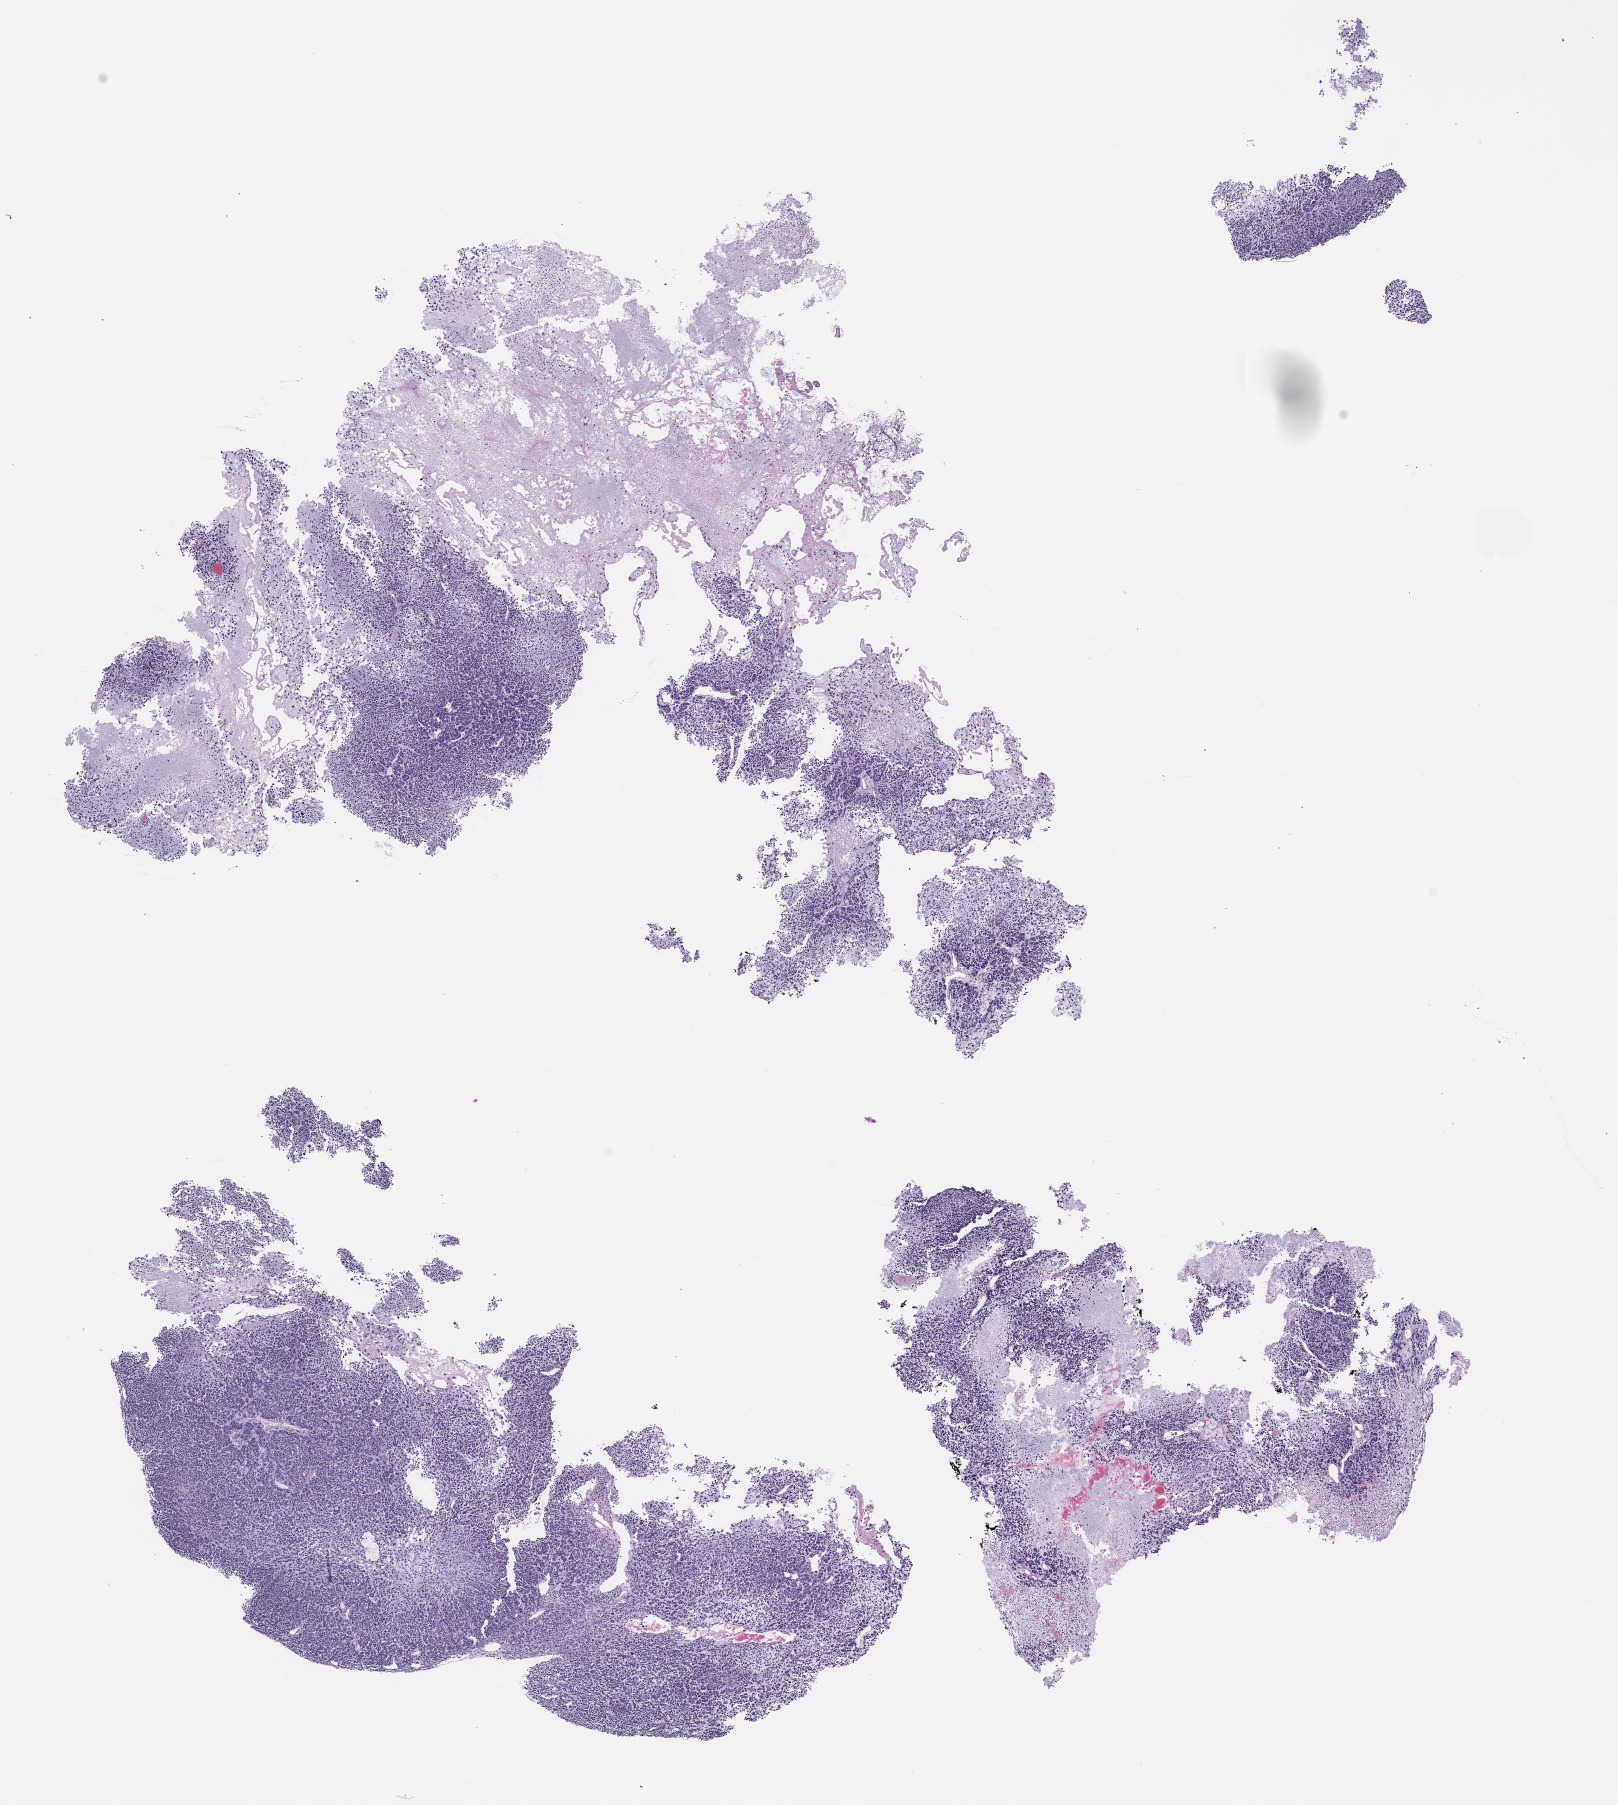
Whole-slide image, haematoxylin and eosin: patient-derived xenograft (human tumor grown in a mouse), passage 2, whole scanned area (about 13.0 x 14.5 mm) shown as a low-resolution overview. Formalin-fixed, paraffin-embedded (FFPE) tissue. Originating tumor site category: bladder.
Originating patient diagnosis: Urothelial Carcinoma.